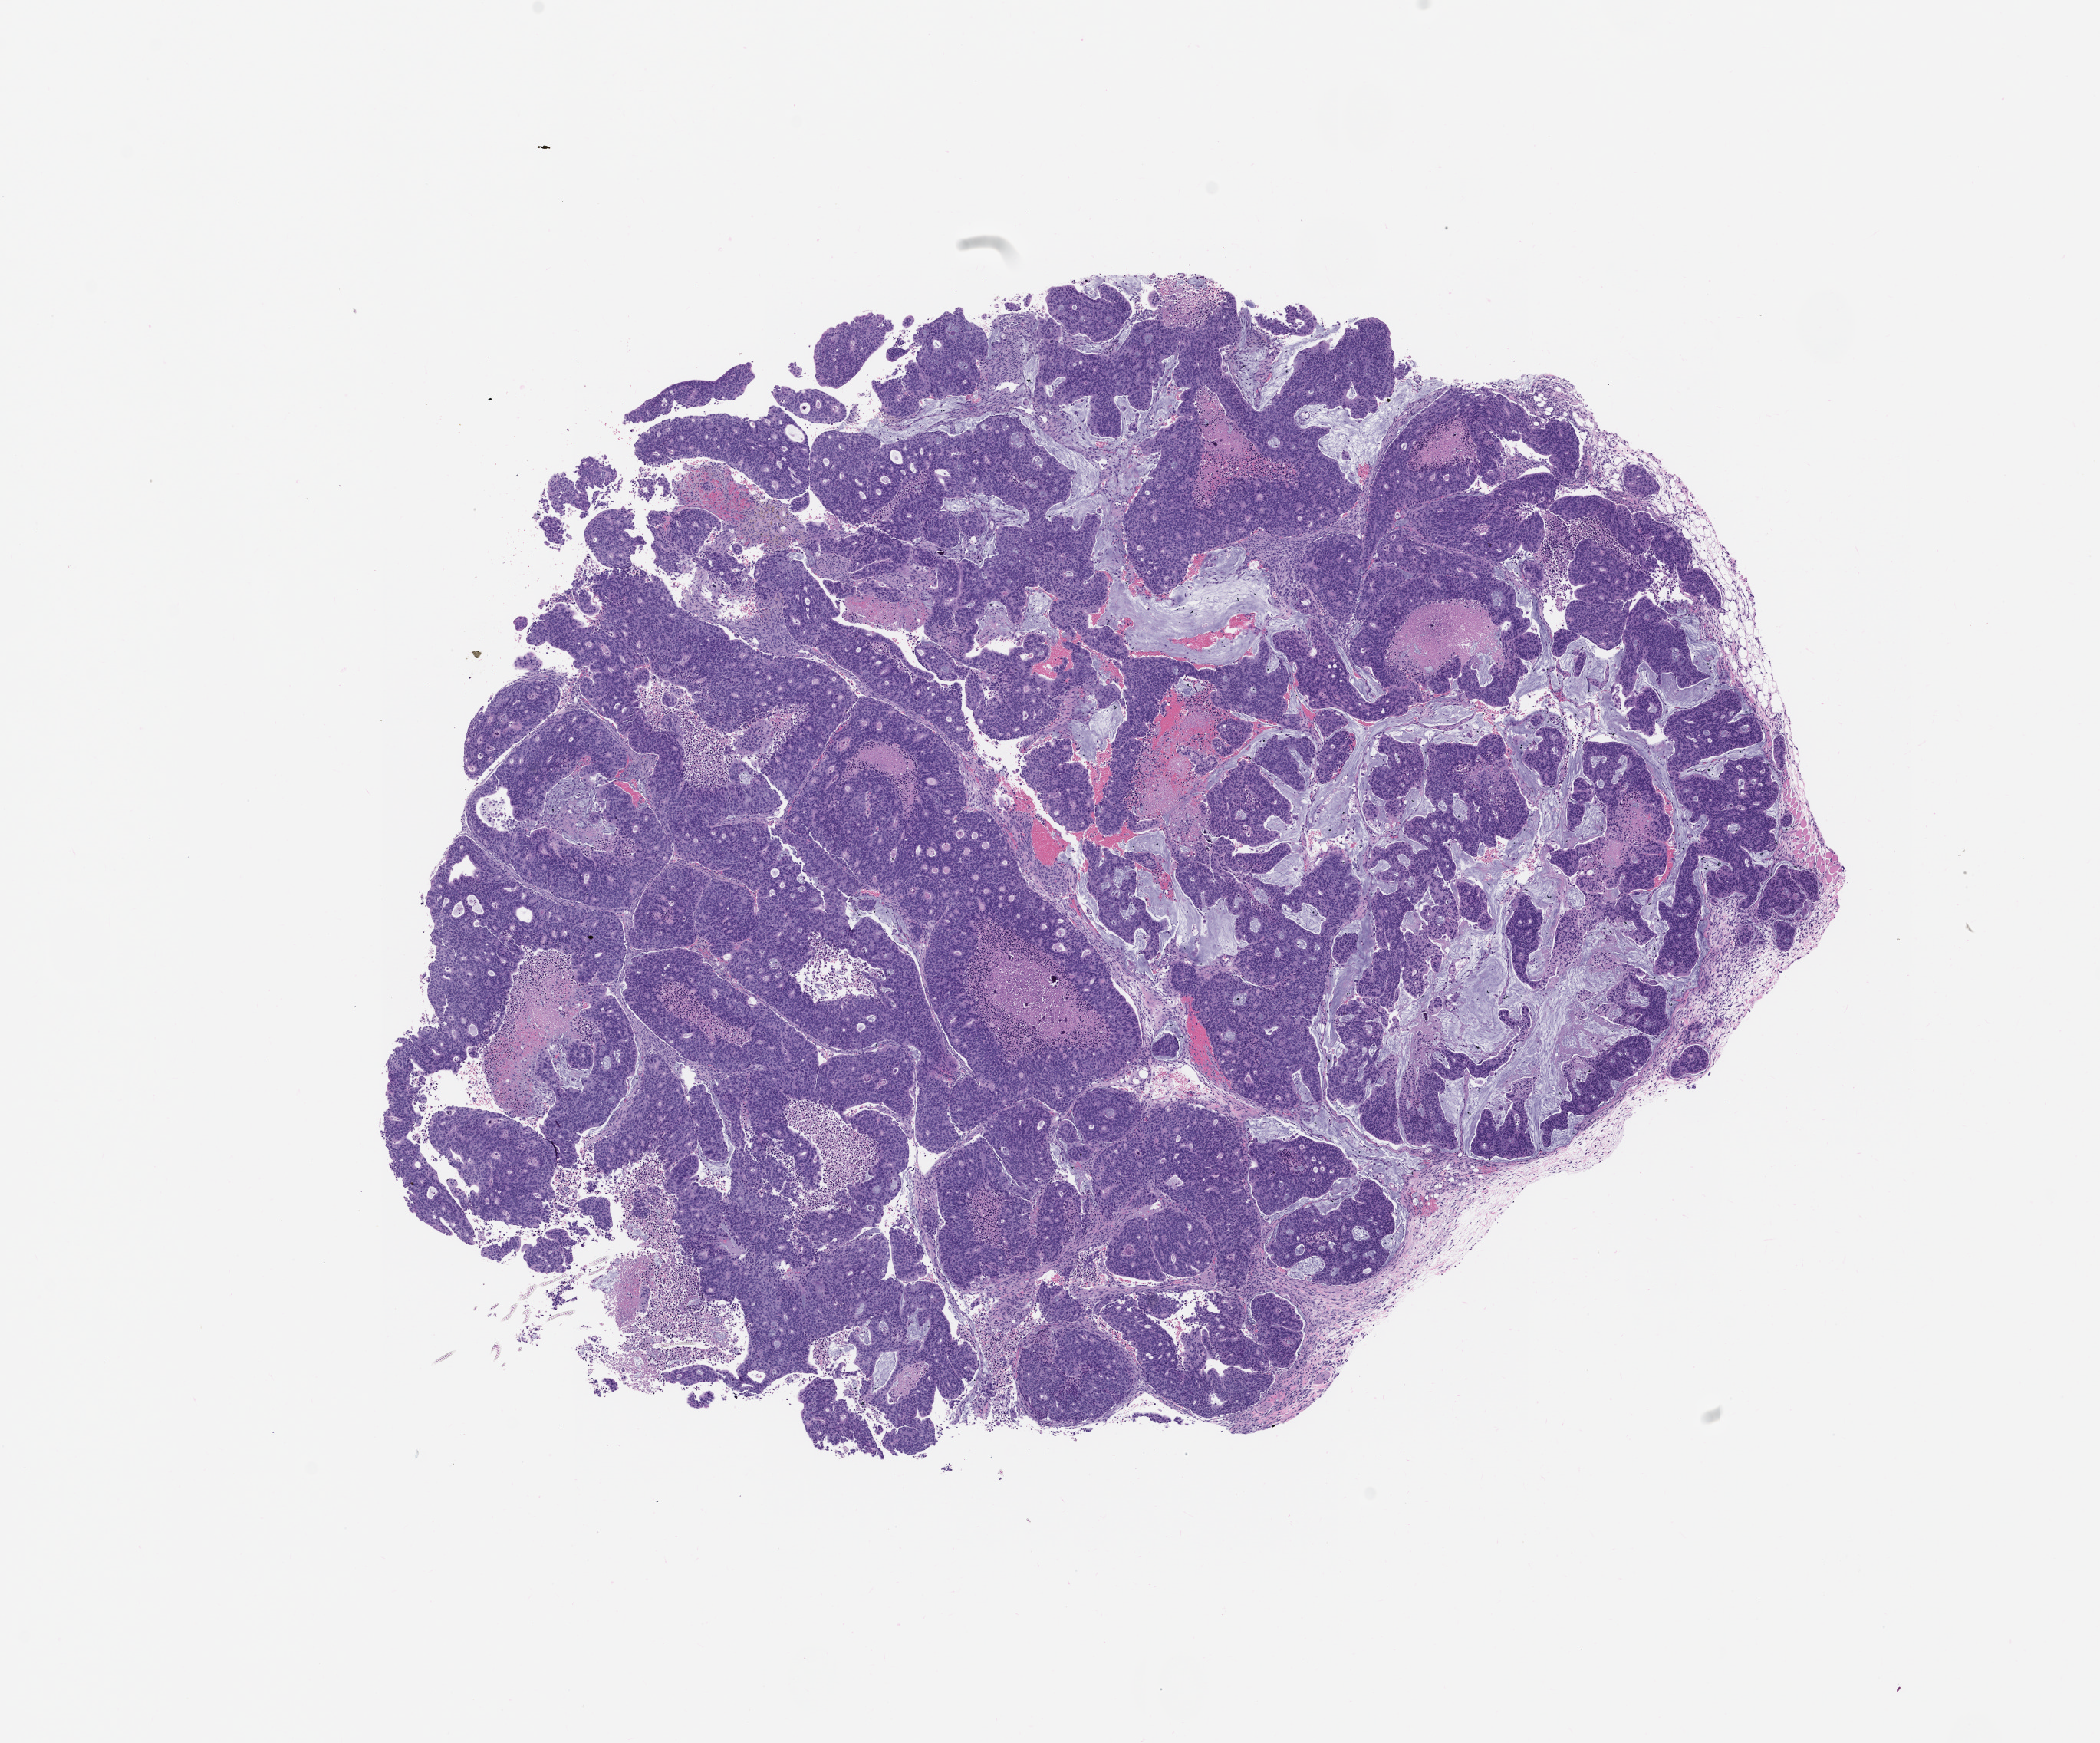
Haematoxylin and eosin whole-slide image of a patient-derived xenograft (PDX) tumor grown in a mouse, passage 1 — shown as a low-resolution overview of the whole scanned area (about 11.0 x 9.1 mm); formalin-fixed paraffin-embedded section; tumor site category: colon.
• originating patient diagnosis: Colon Adenocarcinoma